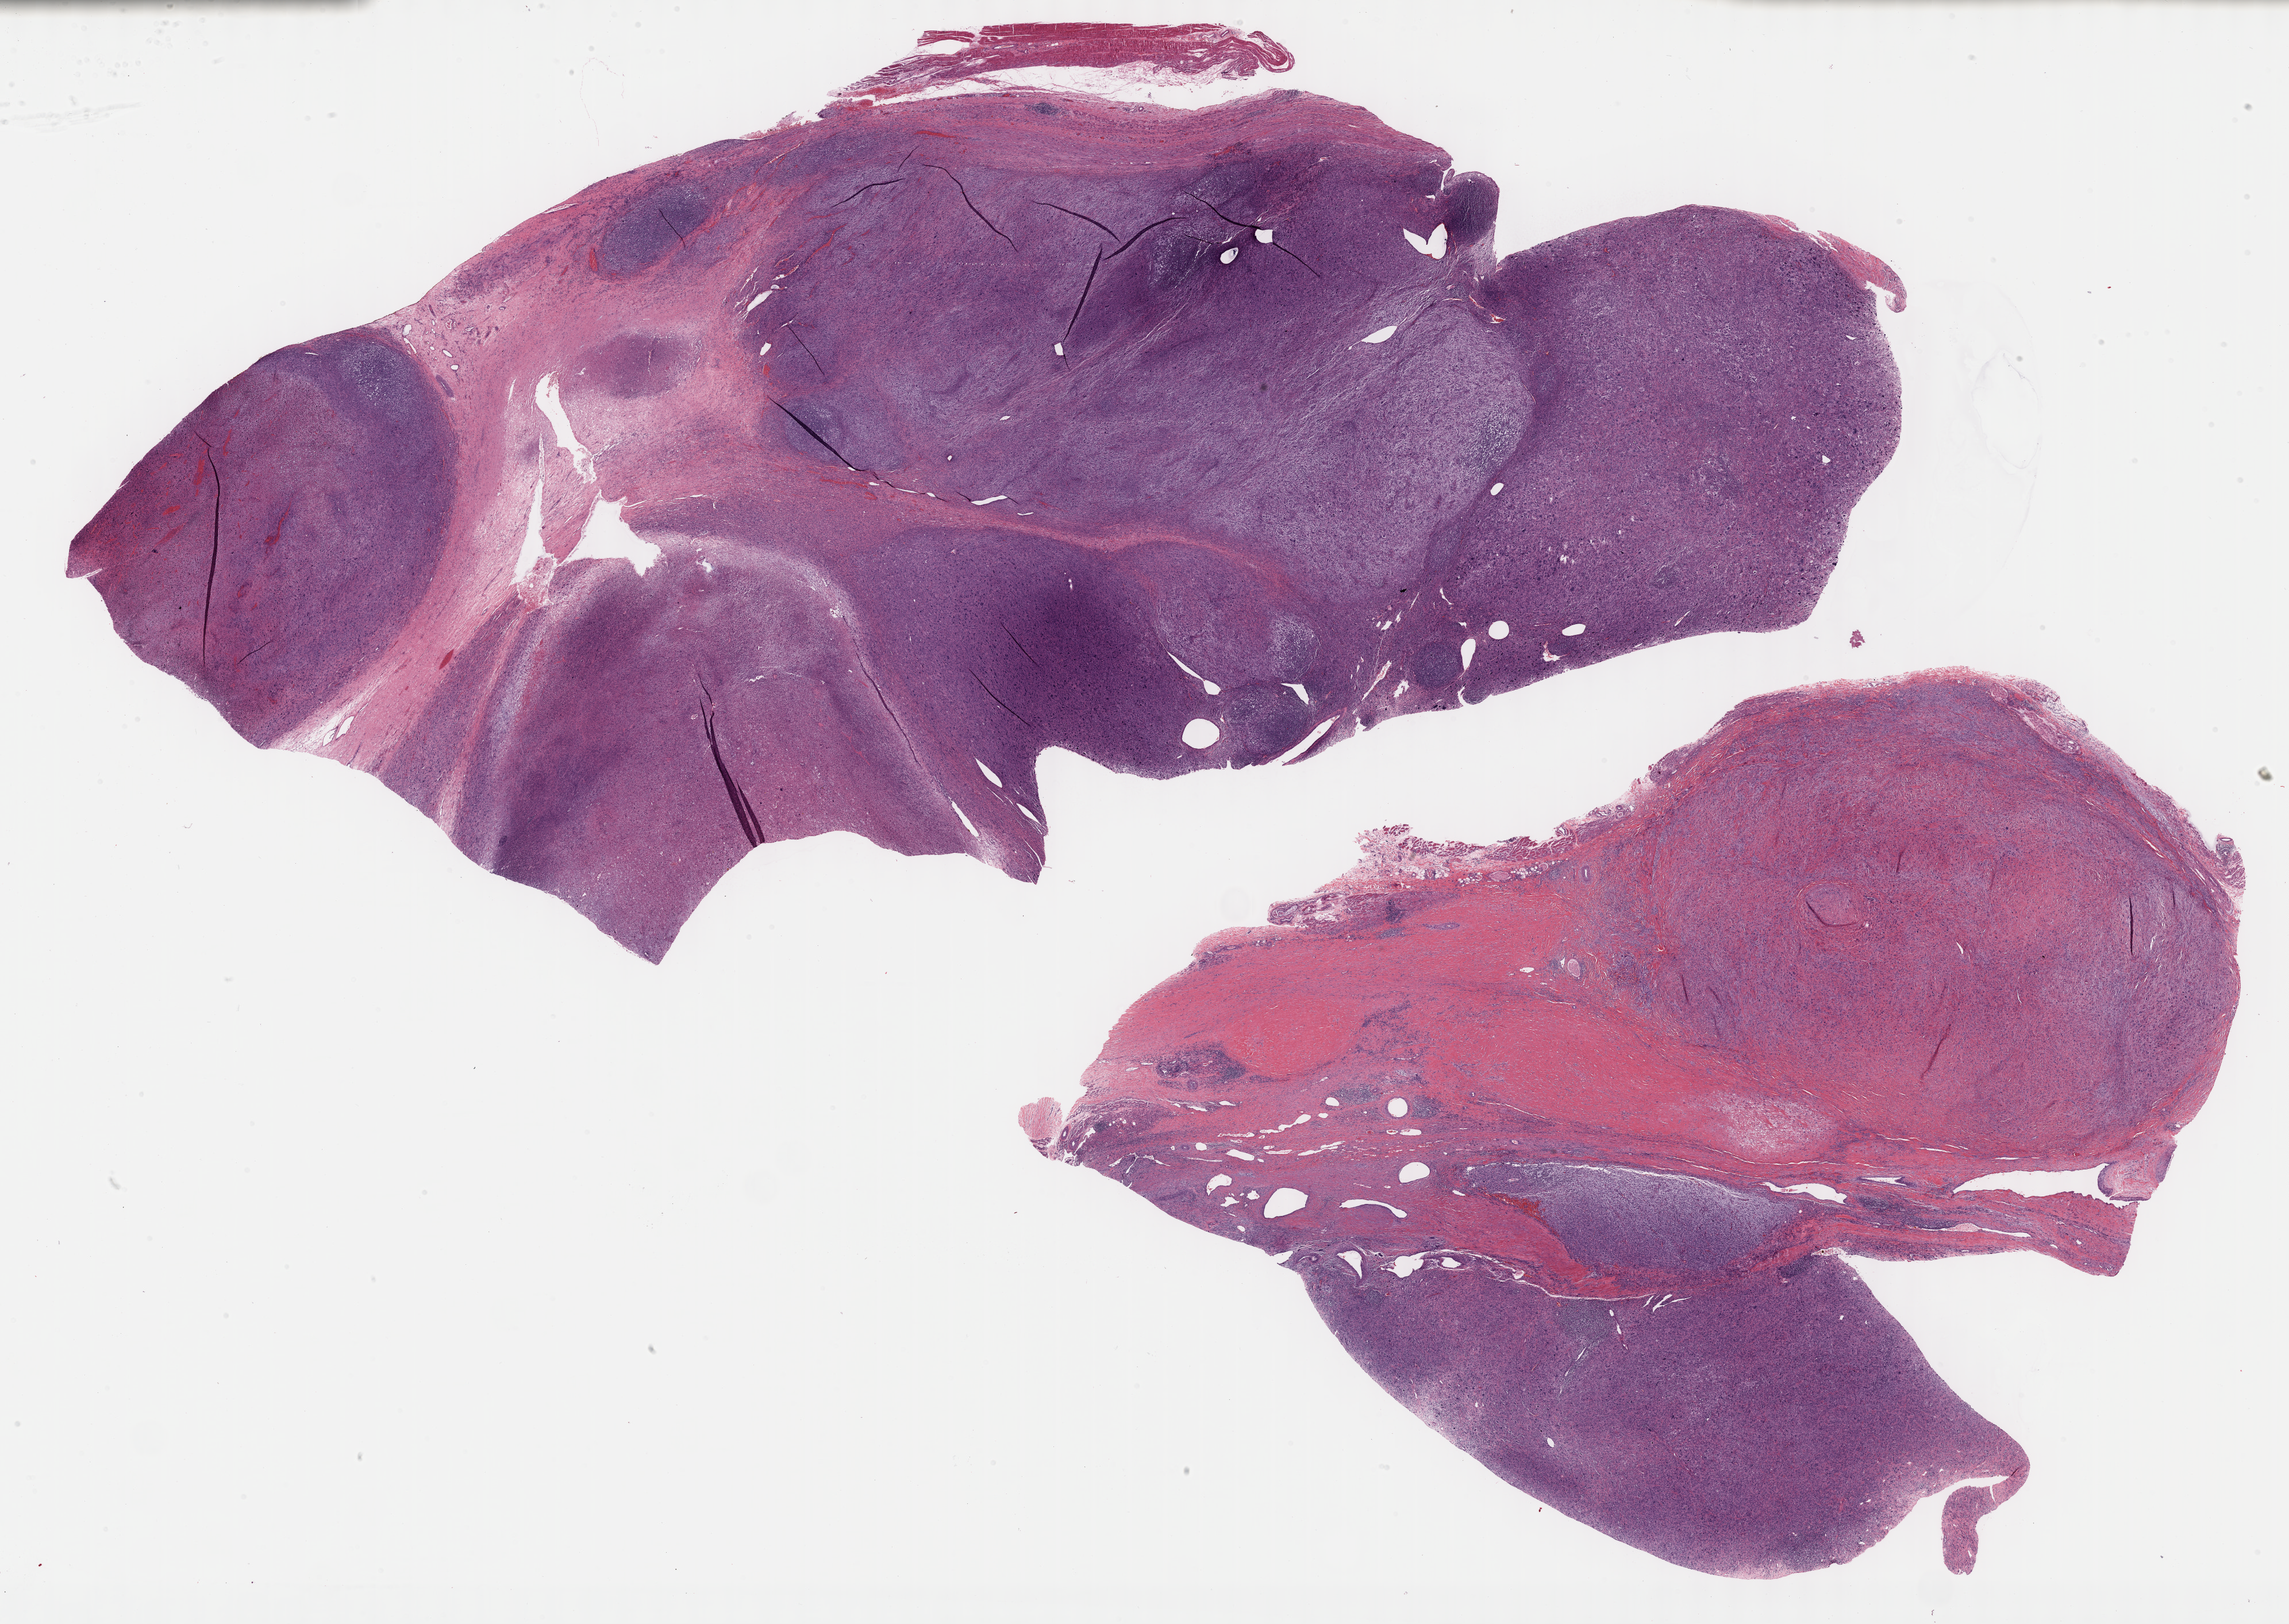
Whole-slide histology image, Hematoxylin and eosin (H&E) stained — a low-resolution overview of the entire scanned area, about 32.2 x 22.9 mm (from a 40x scan), formalin-fixed paraffin-embedded (FFPE) diagnostic section, connective, subcutaneous and other soft tissues, primary tumour sample. Patient: male, age at initial diagnosis 51 years.
Pathologic diagnosis: Fibromyxosarcoma (connective, subcutaneous and other soft tissues of thorax).